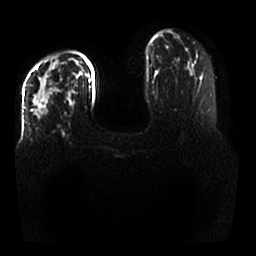
Breast MRI, one axial slice. Position 15 of 25 along the scan axis. Diffusion-weighted series; image 2 of 4 stored at this slice position (different b-values; order by instance number). 1.5 T. 4 mm slice thickness. 256 × 256 image matrix, field of view 350 × 350 mm. Female patient.
Outlined on this slice (expert manual segmentation):
- tumour on diffusion-weighted imaging: bounding box [x1, y1, x2, y2] px = [31, 61, 59, 118]